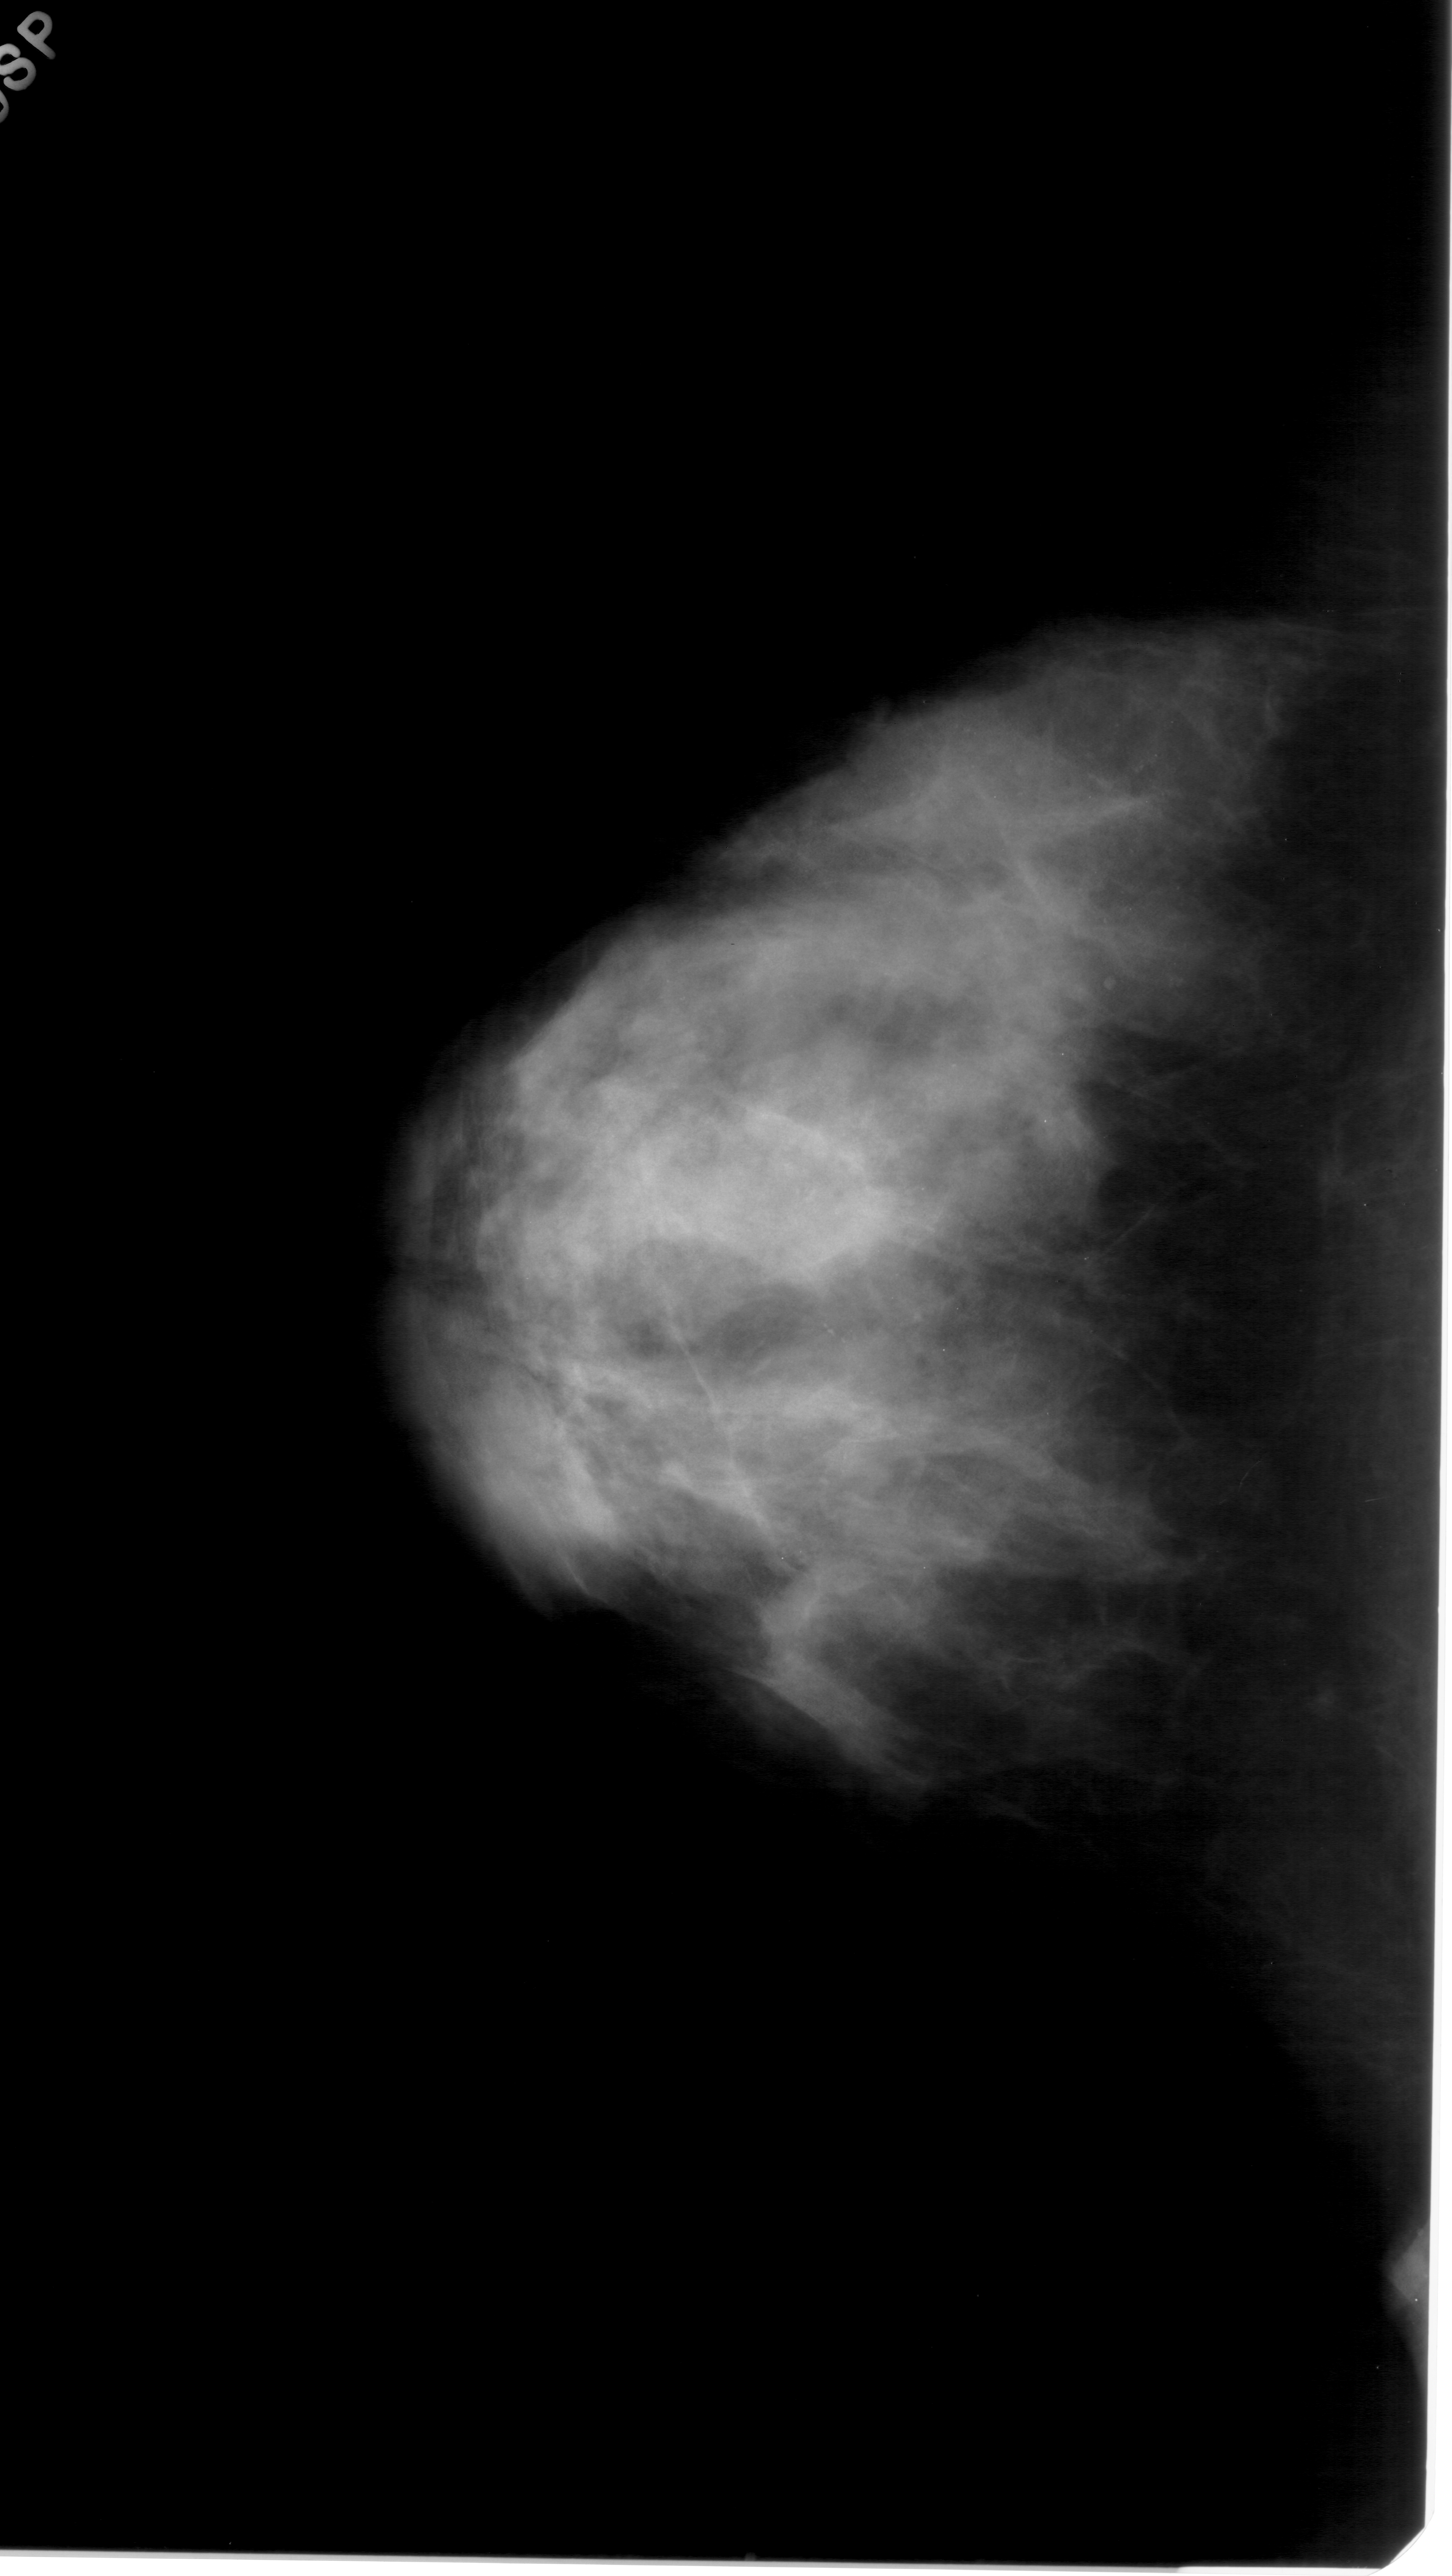
Scanned film-screen mammogram; left breast; craniocaudal (CC) view; 1452 × 2576 image matrix.
Expert-marked regions of interest on this film, with their recorded descriptors:
- calcifications, morphology pleomorphic, distribution clustered; BI-RADS assessment category 4; pathology result (as recorded, not read from the image): benign: bounding box (x1, y1, x2, y2) in pixels: (812, 1306, 874, 1361)